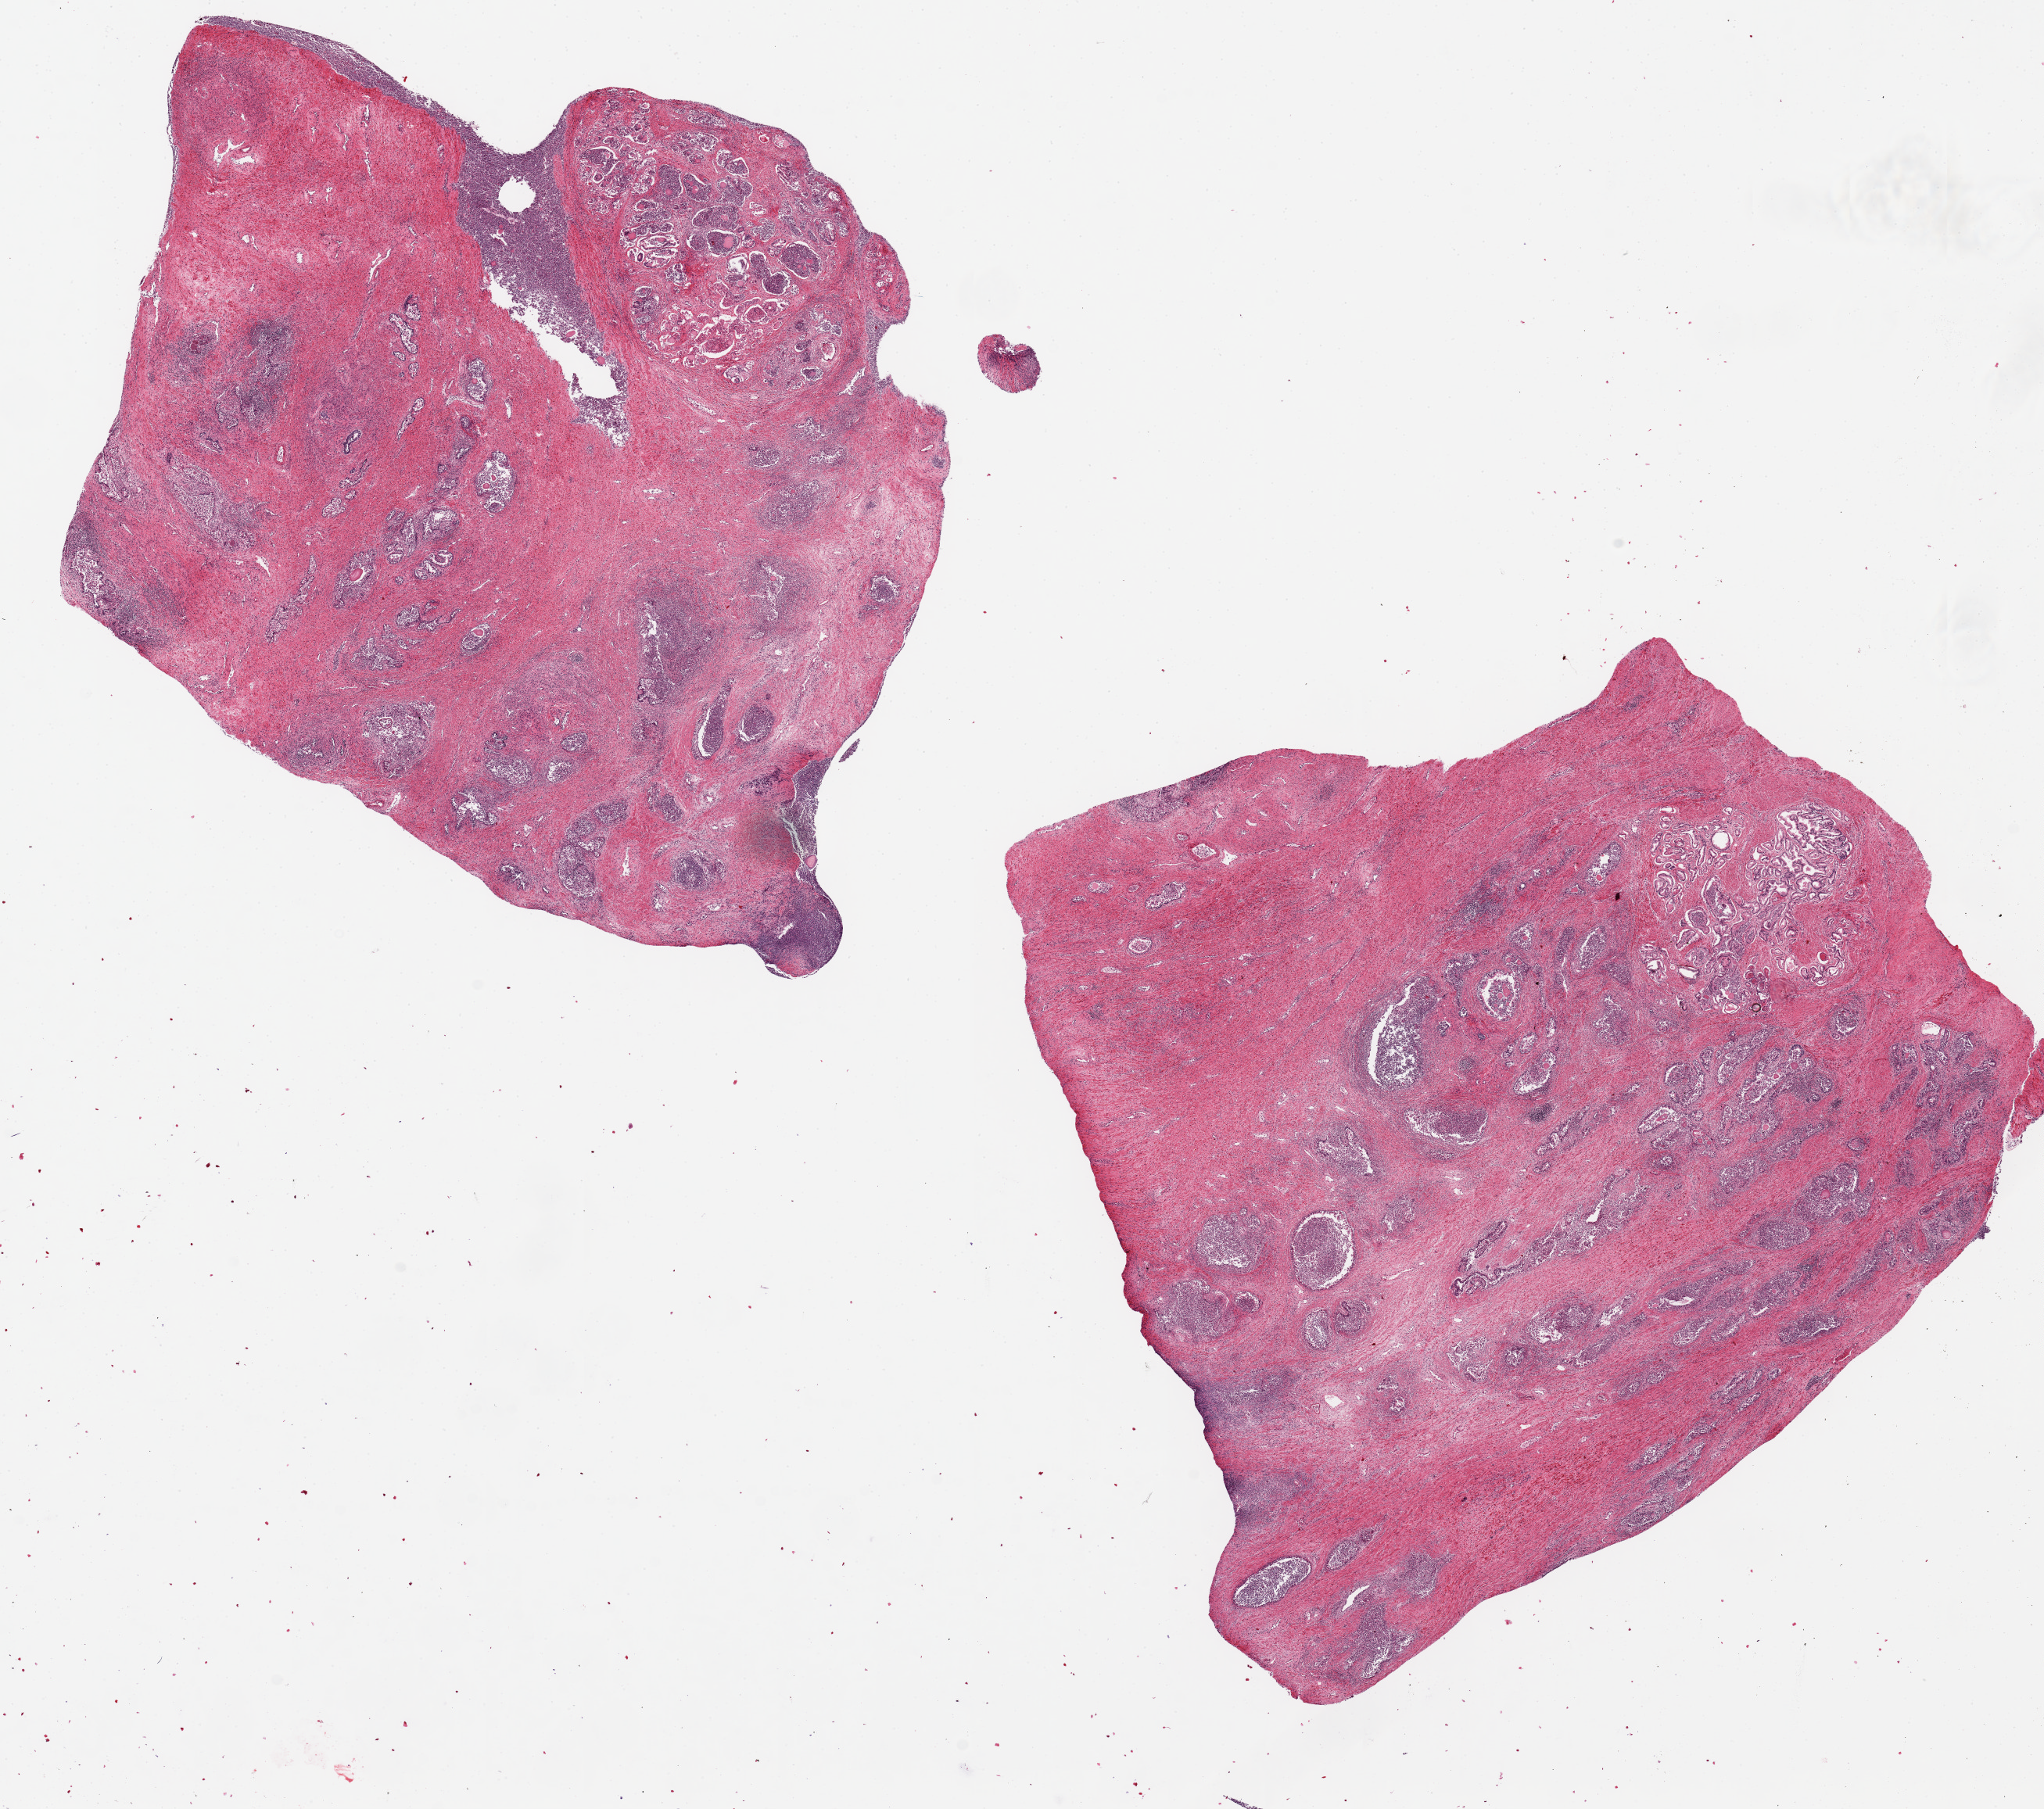
Whole-slide image, haematoxylin and eosin stain, brightfield, shown as a low-resolution overview of the whole scanned area (about 20.7 x 18.3 mm). PAXgene-fixed paraffin-embedded (PFPE) section. Section of prostate (target tissue). Tissue donor sample. Male donor.
Pathologist's review note for this sample: 2 pieces ~9x8mm; Moderate-severe glandular autolysis, diffuse acute and chronic prostatitis, areas.